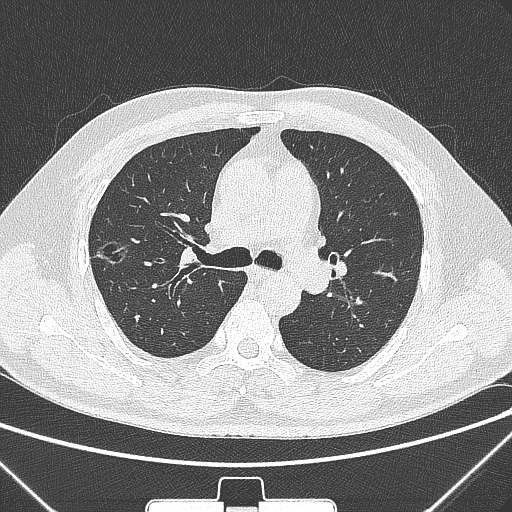
Chest CT, one axial slice; lung window (W 1500 / L -600 HU); 512 × 512 image matrix, field of view 350 × 350 mm. Male patient, age 58 years. Case-level facts recorded for this patient, not image findings: clinical TNM (as recorded): T1c N0 M0; histopathological grade: G2.
Structures marked on this image (bounding box drawn by a radiologist):
- lung tumour (recorded histology: adenocarcinoma): bounding box (x1, y1, x2, y2) in pixels: (88, 227, 142, 277)